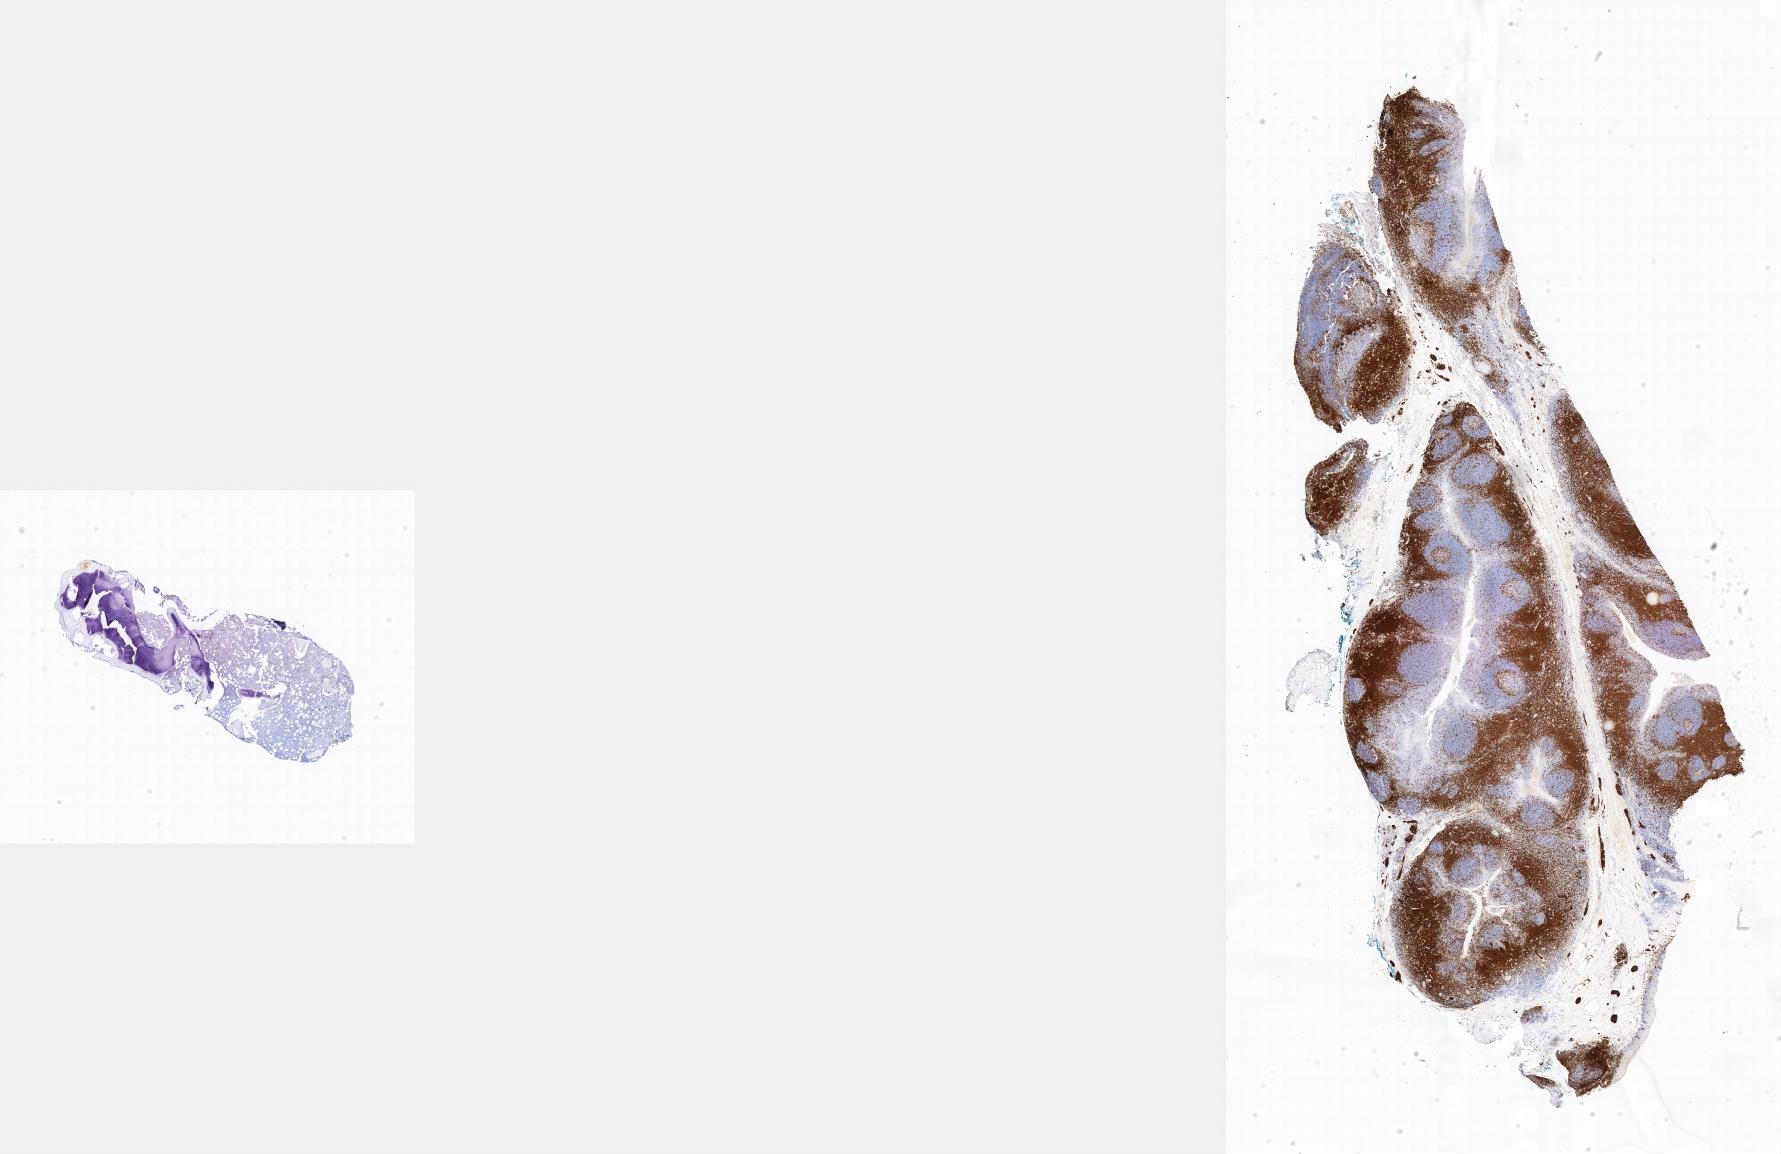
Immunohistochemistry (IHC) whole-slide image stained for CD3, a low-resolution overview of the entire scanned area. Specimen: tumor tissue. Anatomic site: bone marrow. Patient: male, aged 15.
Histologic diagnosis: Burkitt lymphoma, NOS.